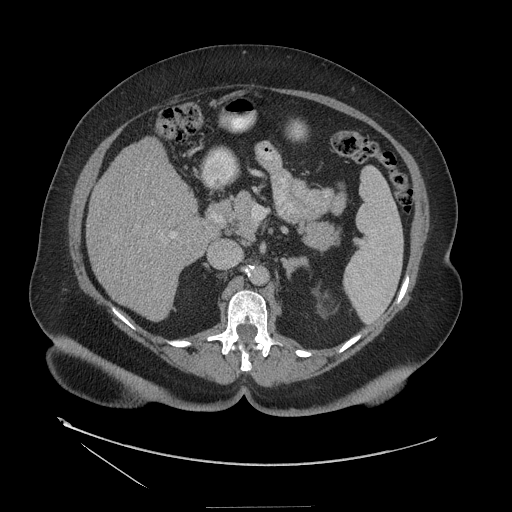
Contrast-enhanced abdominal CT (liver protocol), one axial slice. Slice 63 of 127 in the series (ordered by position). Reconstruction kernel STANDARD. 140 kVp. Soft-tissue window (W 400 / L 40 HU). 2.5 mm slice thickness. 512 × 512 image matrix. From the clinical record (not read from this slice): diagnosis: hepatocellular carcinoma (patient treated with transarterial chemoembolisation; whether this scan precedes or follows treatment is not stated here); TNM stage (as recorded): Stage-II; Child-Pugh class: A; tumour size: 3 cm.
Annotated regions visible in this slice (semi-automatic segmentation, software-assisted and operator-edited):
- liver parenchyma outside the tumour (the mass and vessels are separate outlines, so this box may not span the whole liver): bounding box <86,138,212,320> (left, top, right, bottom; pixels)